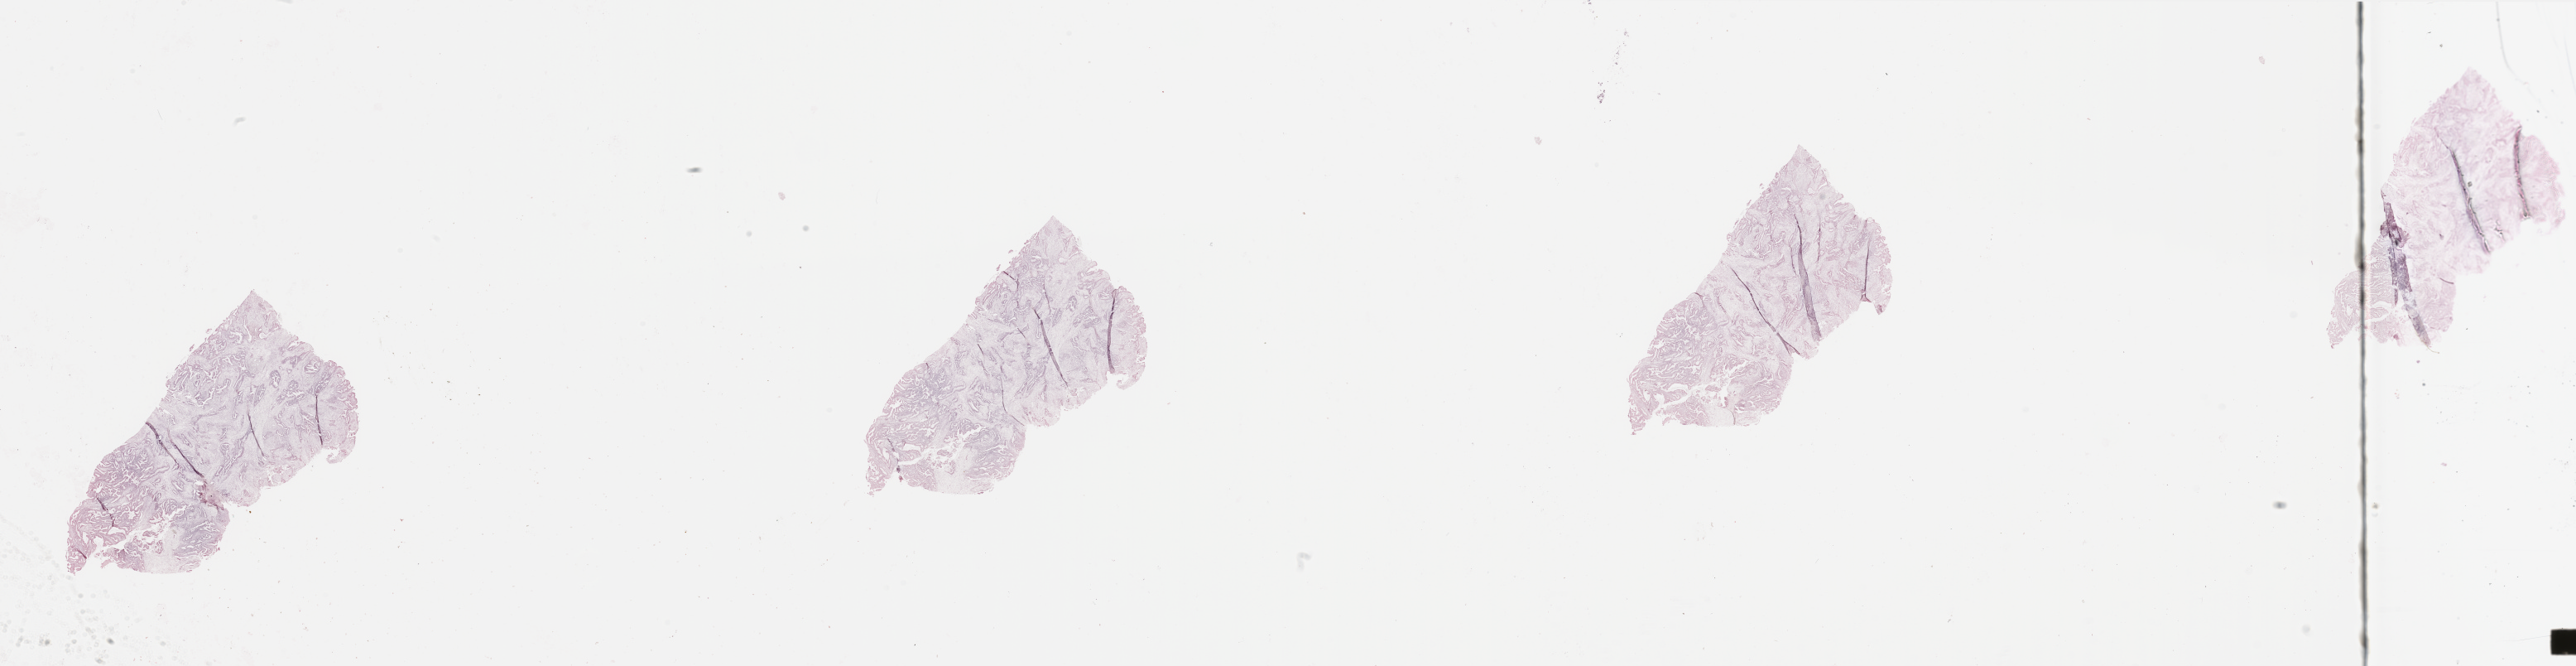
Whole-slide histology image, H&E-stained, low-resolution overview of the scanned area, about 49.2 x 12.7 mm (slide scanned at 20x), uterus, tumour tissue. Female, 58 y/o. Histologic grade: G1 (well differentiated).
AJCC pathologic stage: III. Primary tumour site (as recorded): posterior endometrium. Histologic diagnosis: Endometrioid adenocarcinoma, NOS.